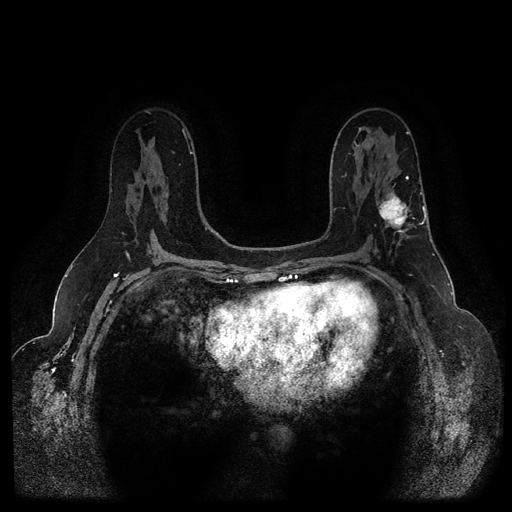
Breast MRI (dynamic contrast-enhanced, multi-phase), one axial slice; slice 60 of 116 in the series (ordered by position); dynamic contrast-enhanced series, time point 2 of 5 at this slice position (early post-contrast); 1.5 T; TE 2.6 ms, TR 5.3 ms; 512 × 512 image matrix. Patient: female, 54 years.
Outlined on this slice (semi-automatic segmentation, software-assisted and operator-edited):
- breast lesion (labelled 'tumour' in the annotation; benign lesions carry a separate 'benign' label): bounding box <376,188,413,231> (left, top, right, bottom; pixels)